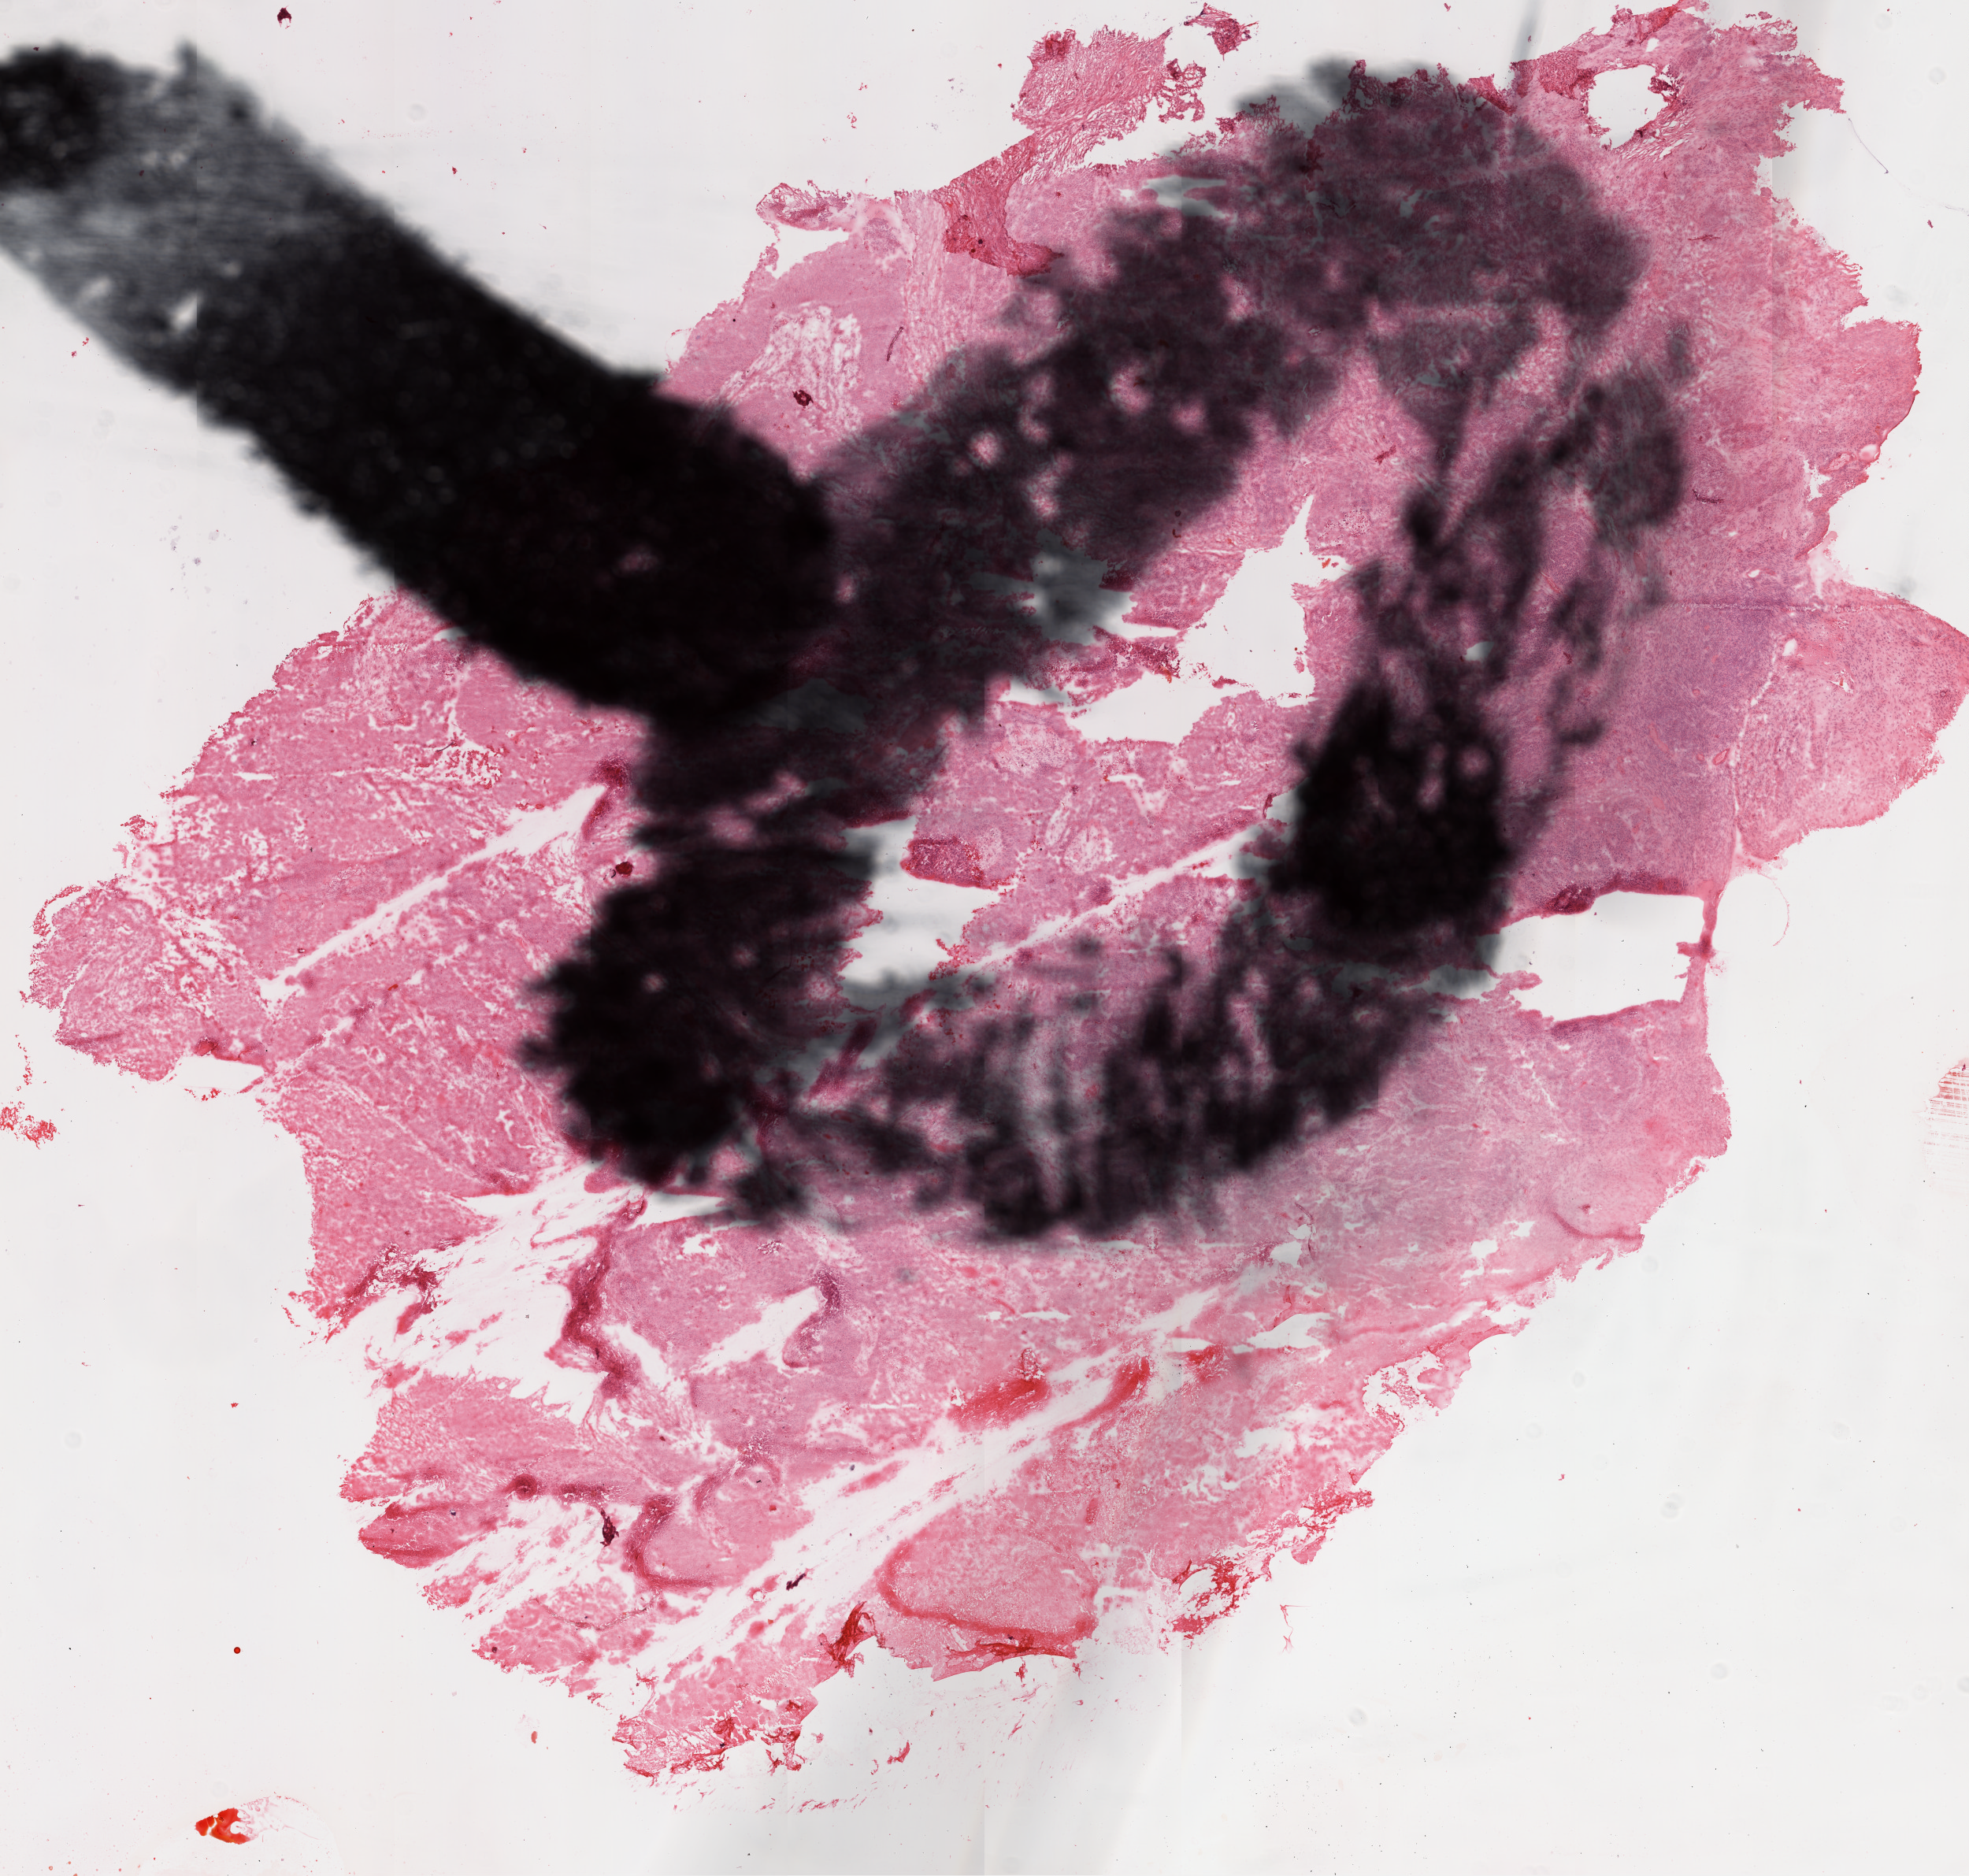
H&E whole-slide image — a low-resolution overview of the entire scanned area, about 10.0 x 9.6 mm (slide scanned at 20x); frozen section from the top of the tissue portion; primary tumour sample from the ovary. Female, age 42 years at initial diagnosis. Histologic grade: G3 (poorly differentiated). Pathologist review of this section (percent, as recorded): tumour cells 90%, tumour nuclei 90%, normal cells 0%, stromal cells 0%, necrosis 10%.
- laterality: bilateral
- FIGO stage: IV
- pathologic diagnosis: Serous cystadenocarcinoma, NOS